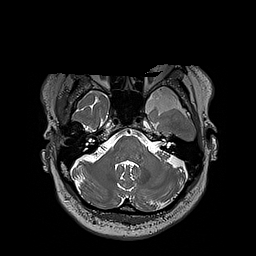
Brain MRI from a brain-tumour surgery series, one axial slice; slice 151 of 192 in the series (ordered by position); 1 mm slice thickness; 256 × 256 image matrix. From the clinical record (not read from this slice): histopathology: Oligodendroglioma; WHO grade: 3; IDH mutation: yes; tumour location: Left Sylvian Fissure (Temporal).
Structures marked on this image (expert manual segmentation):
- tumour: bounding box [x1, y1, x2, y2] px = [124, 86, 197, 112]